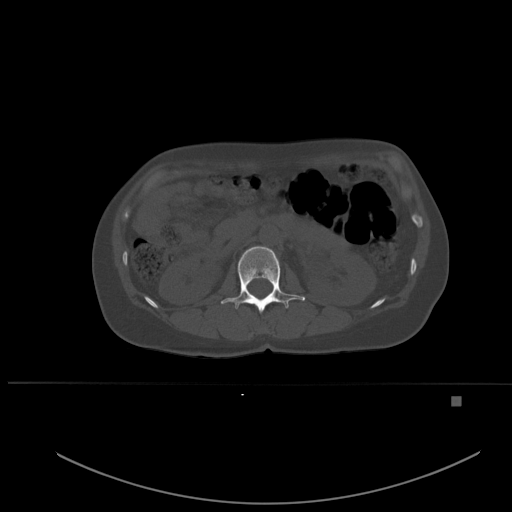
CT including the spine, one axial slice; slice 234 of 651 in the series (ordered by position); bone window (W 1800 / L 400 HU); 1.5 mm slice thickness; 512 × 512 image matrix, field of view 443 × 443 mm. Female patient, age 49 years. From the clinical record (not read from this slice): primary cancer: breast; vertebrae with lytic lesions (as recorded): L3, T12, L4.
Outlined on this slice (semi-automatic segmentation, software-assisted and operator-edited):
- L1 vertebra: box from (x=221, y=246) to (x=305, y=313) px